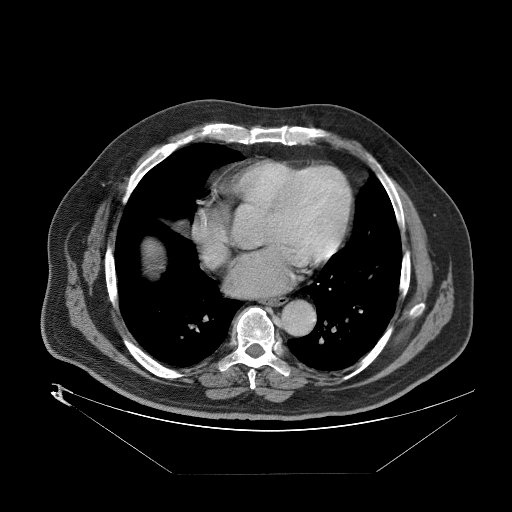
Contrast-enhanced abdominal CT (liver protocol), one axial slice. Position 87 of 89 along the scan axis. Reconstruction kernel STANDARD. 140 kVp. One of 2 acquisitions stored at this slice position. Soft-tissue window (W 400 / L 40 HU). 2.5 mm slice thickness. 512 × 512 image matrix. From the clinical record (not read from this slice): diagnosis: hepatocellular carcinoma (patient treated with transarterial chemoembolisation; whether this scan precedes or follows treatment is not stated here); TNM stage (as recorded): Stage-II; Child-Pugh class: B; tumour differentiation: moderately differentiated; tumour nodularity: multinodular.
Structures marked on this image (semi-automatic segmentation, software-assisted and operator-edited):
- abdominal aorta: bounding box (x1, y1, x2, y2) in pixels: (280, 301, 313, 336)